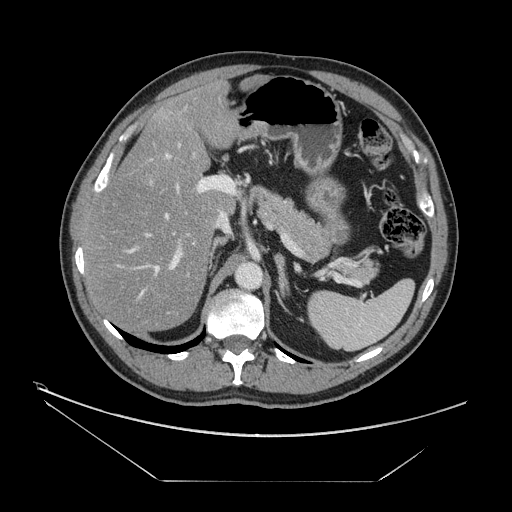
Contrast-enhanced abdominal CT, one axial slice. Slice 91 of 161 in the series (ordered by position). Reconstruction kernel STANDARD. Intravenous contrast given. Soft-tissue window (W 400 / L 40 HU). 2.5 mm slice thickness. 512 × 512 image matrix, field of view 440 × 440 mm. Male patient, age 65 years. From the clinical record (not read from this slice): diagnosis: colorectal cancer liver metastases, imaged before liver resection; multiple liver metastases: yes; largest metastasis: 4.2 cm; disease in both lobes: yes.
Structures marked on this image (expert manual segmentation):
- hepatic veins: bounding box (x1, y1, x2, y2) in pixels: (116, 180, 180, 298)
- liver: (85, 85, 238, 330)
- planned liver remnant (the part of the liver to remain after resection): (85, 85, 238, 330)
- portal vein (with intrahepatic branches): (123, 153, 234, 314)